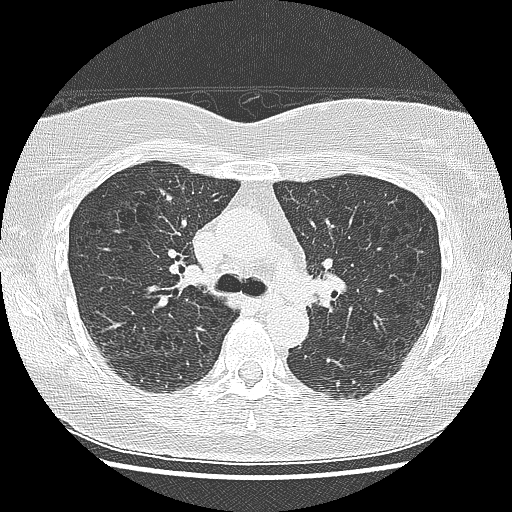
Low-dose screening chest CT, one axial slice; position 99 of 155 along the scan axis; 120 kVp; lung window (W 1500 / L -600 HU); 2.5 mm slice thickness; 512 × 512 image matrix, field of view 330 × 330 mm.
Outlined on this slice (outlined manually by an expert reader):
- lesion 1 (tumor, upper lobe of right lung): bounding box <157,189,175,204> (left, top, right, bottom; pixels)